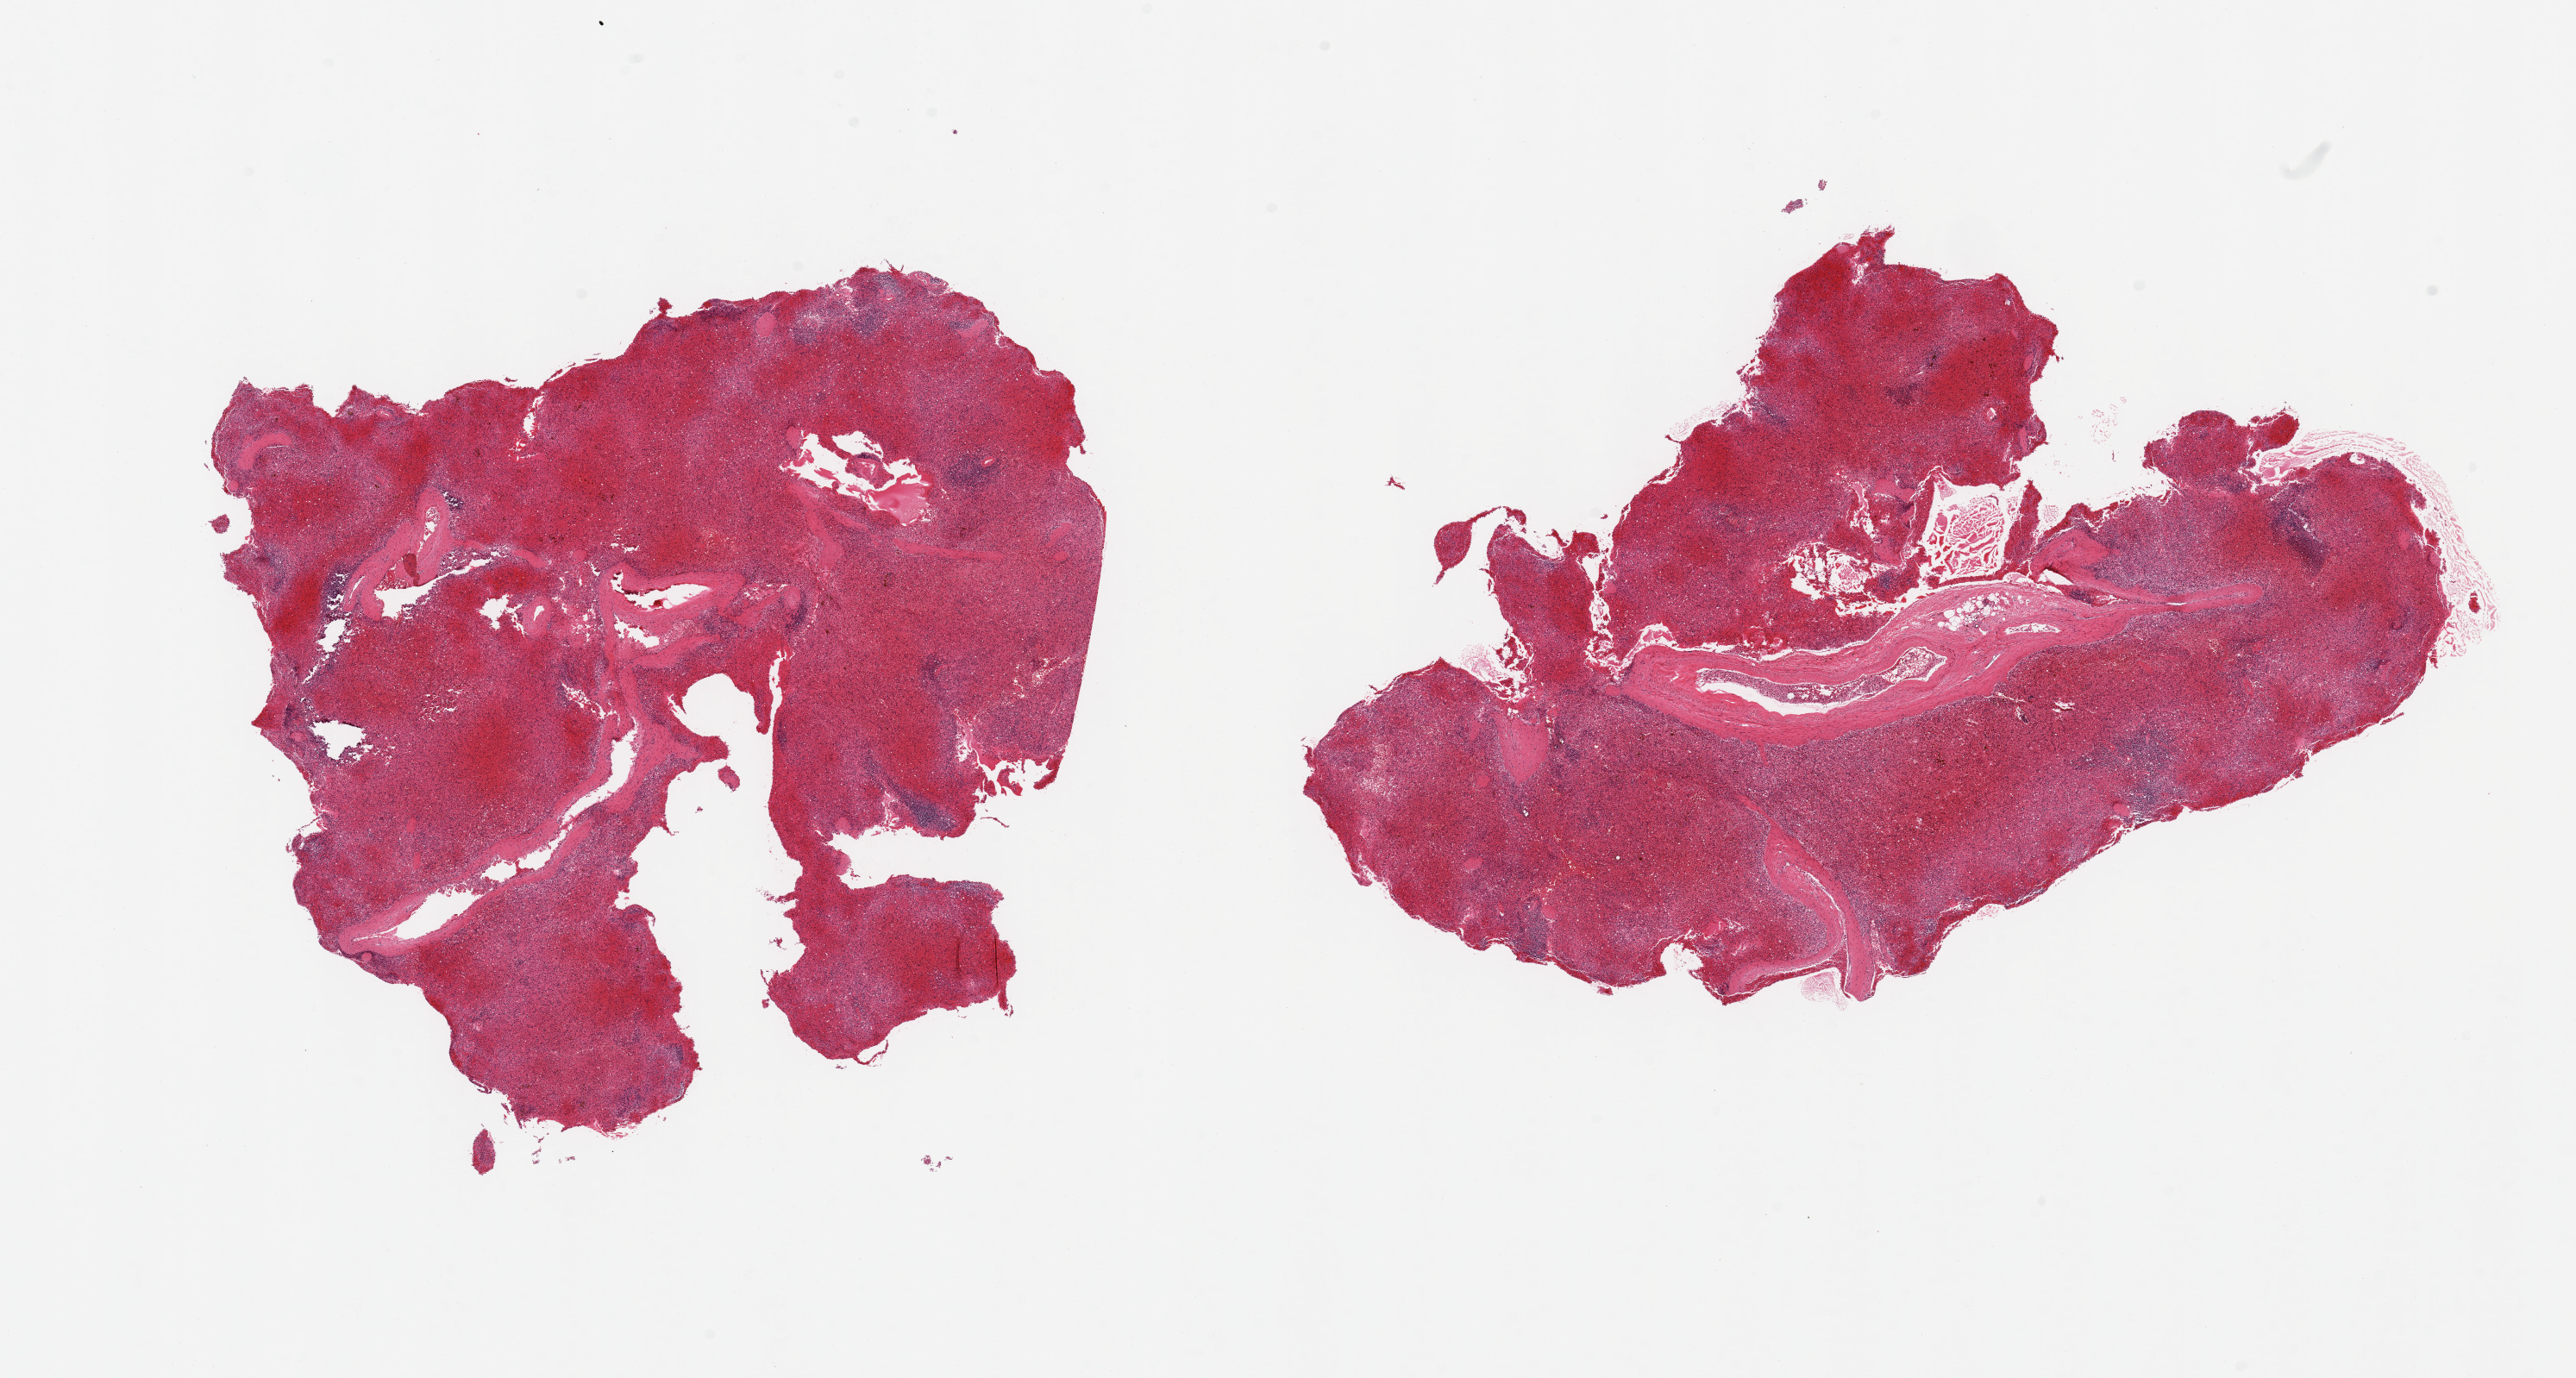
Whole-slide image, hematoxylin and eosin (H&E) stain, a low-resolution overview of the entire scanned area, about 23.6 x 12.6 mm; PAXgene-fixed paraffin-embedded (PFPE) section; section of spleen (target tissue); donor tissue sample.
- review note (as recorded): 2 fragmented pieces; severe vascular congestion